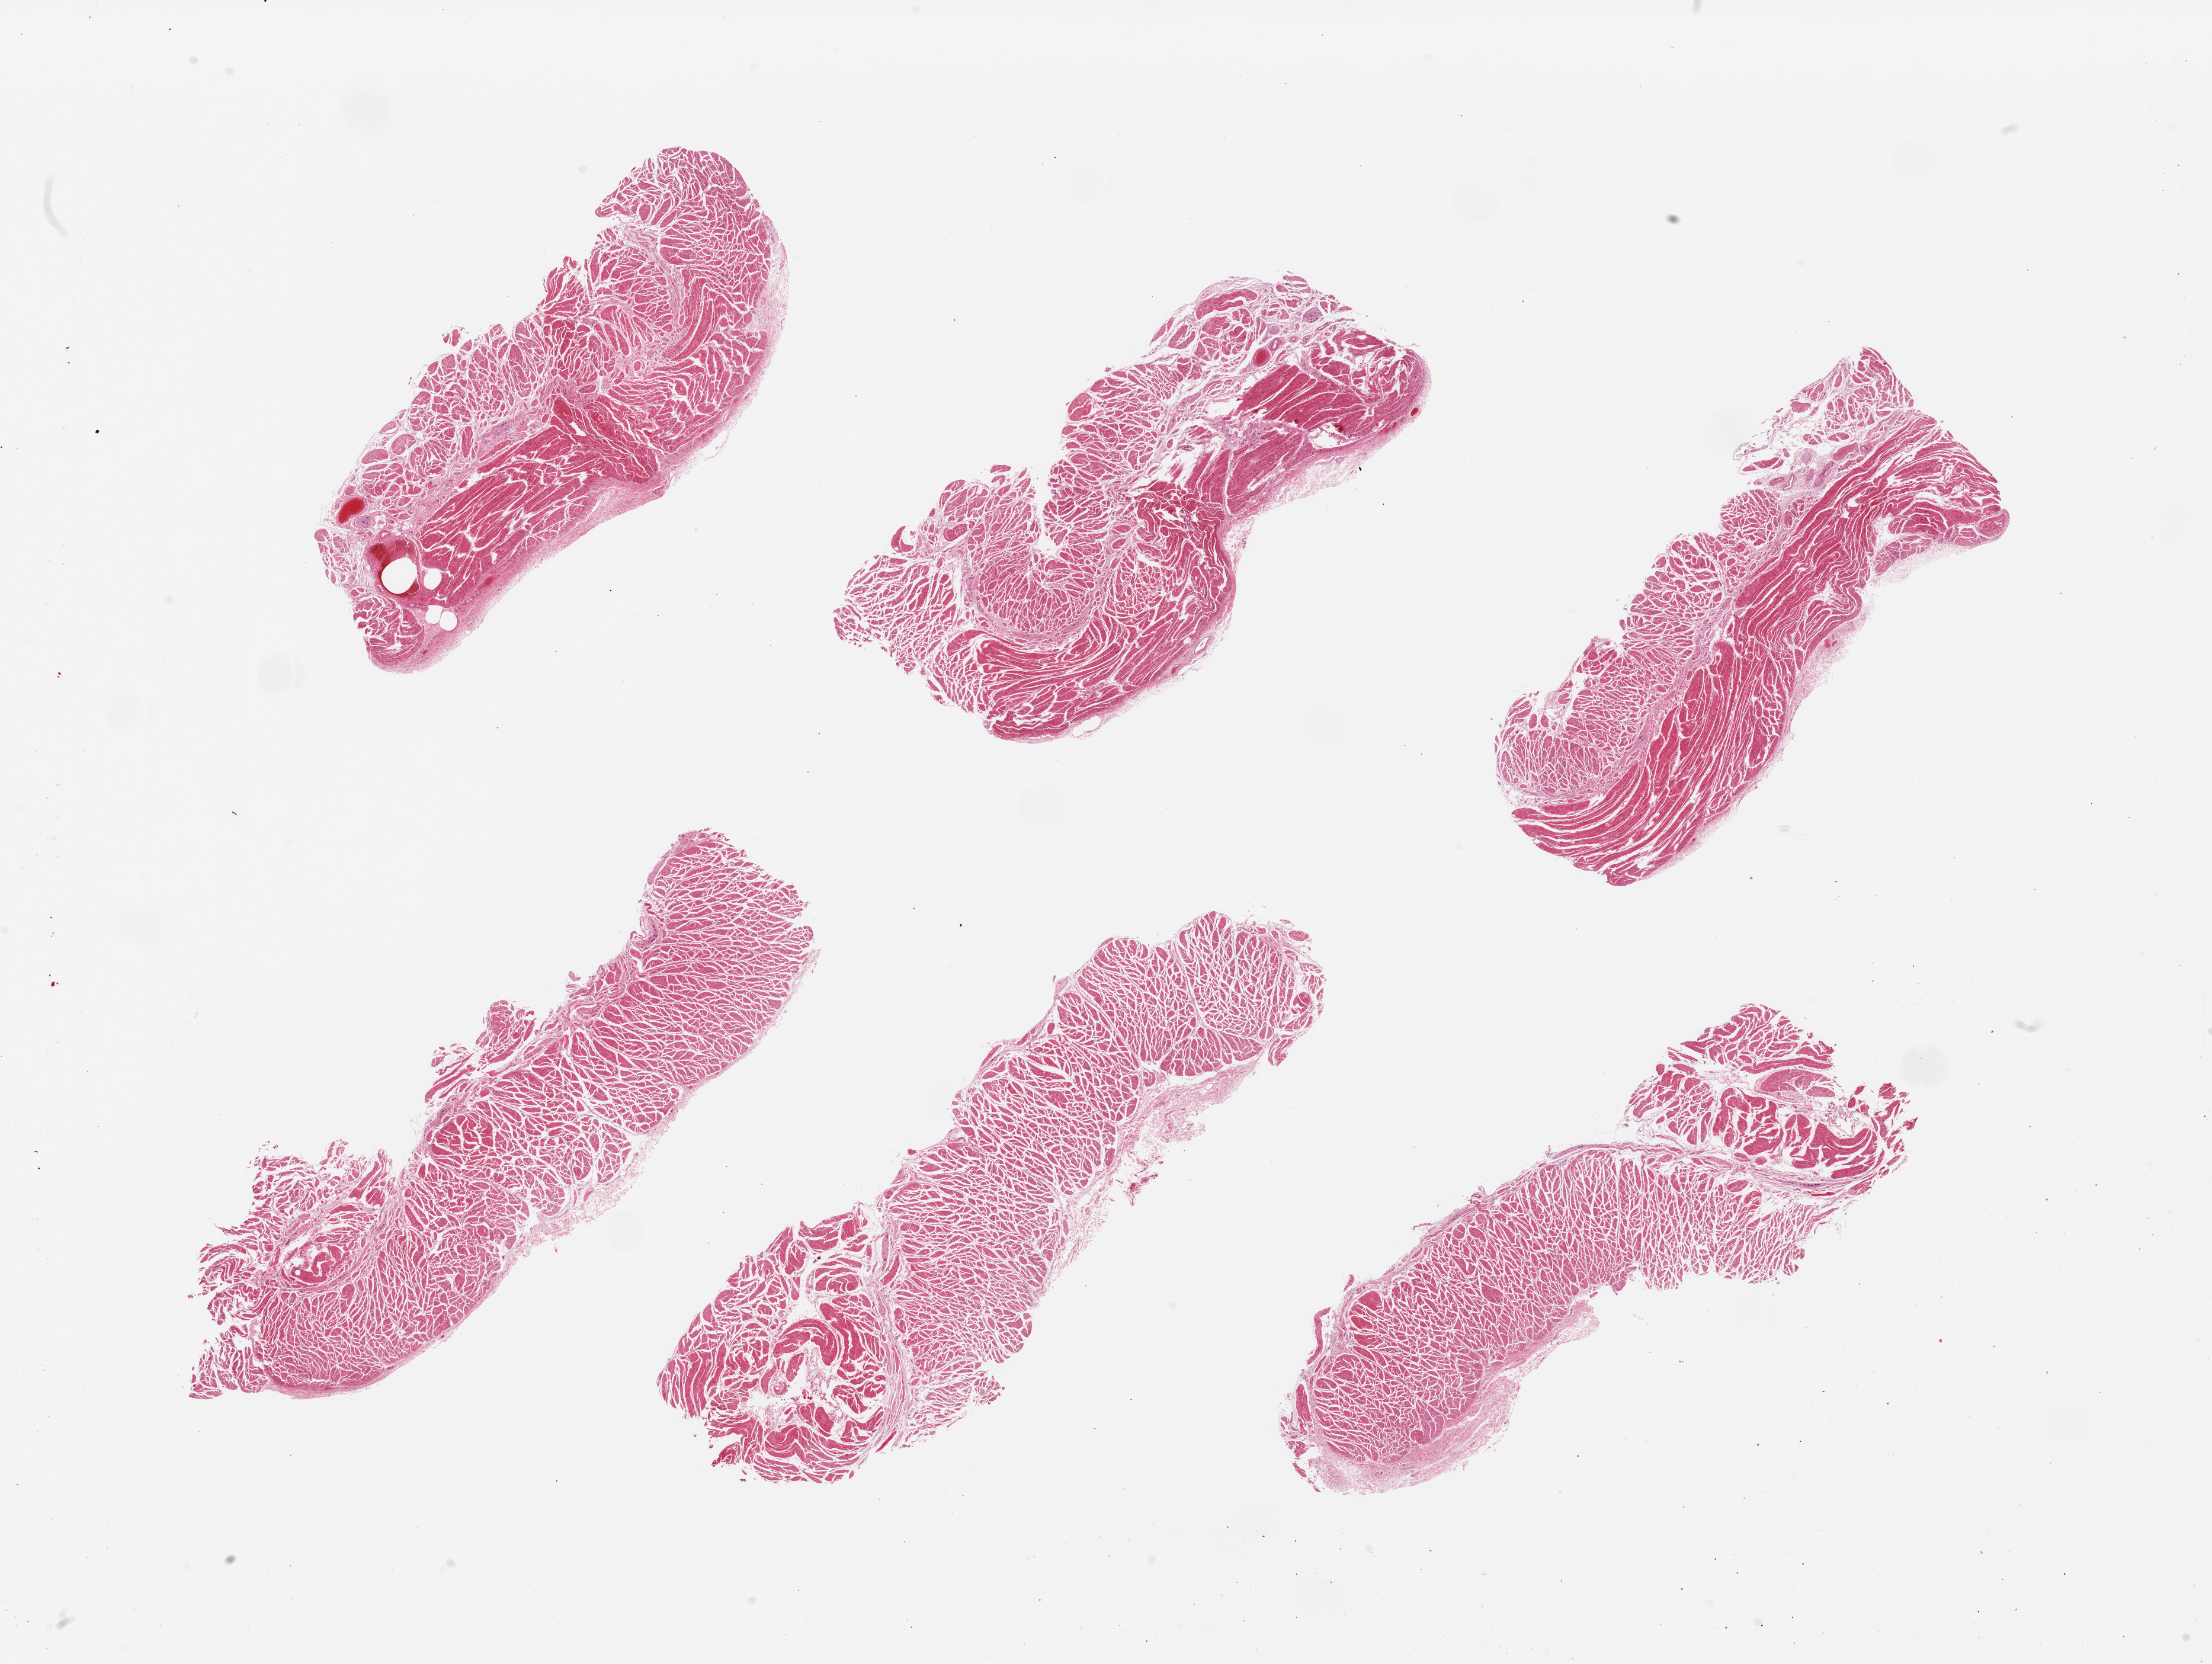
Whole-slide image, haematoxylin and eosin stain, brightfield — shown as a low-resolution overview of the whole scanned area (about 29.5 x 22.2 mm, acquisition: 20x scan); PAXgene-fixed paraffin-embedded (PFPE) section; target tissue: gastroesophageal junction; donor tissue sample.
Review note (as recorded): 6 pieces; well trimmed.